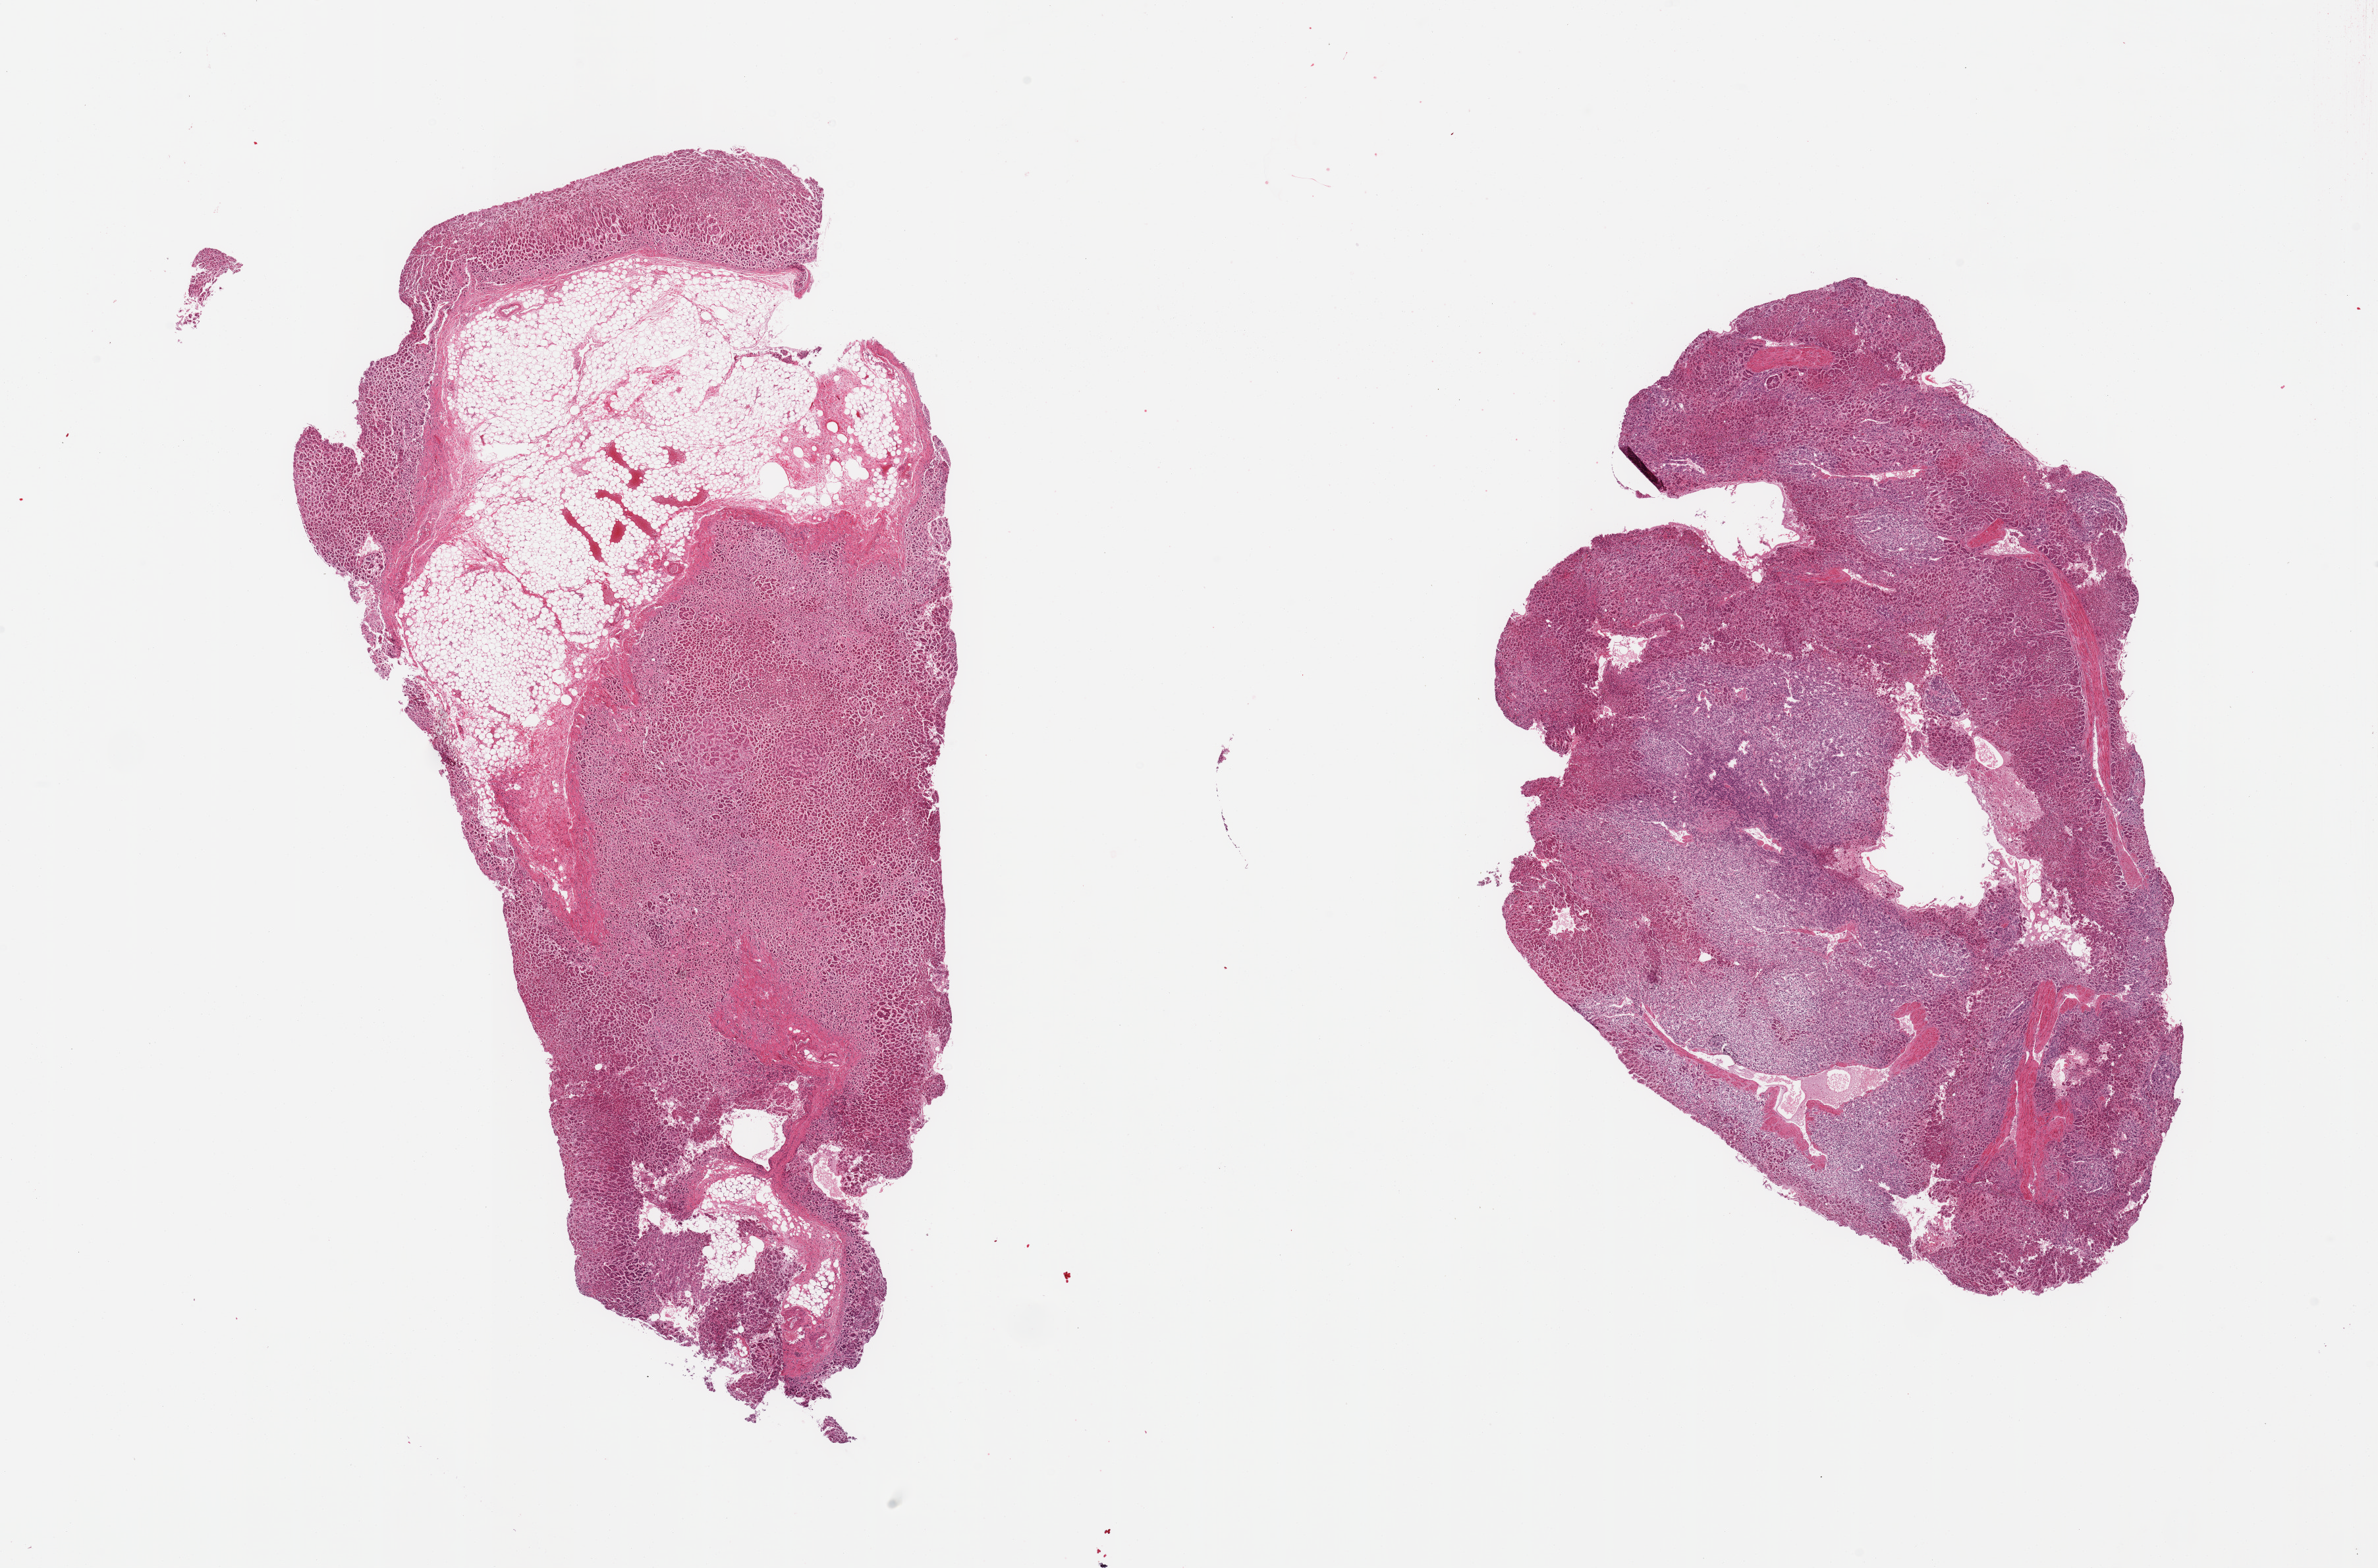
Haematoxylin and eosin whole-slide image, low-resolution overview of the scanned area, about 28.5 x 18.8 mm; PAXgene-fixed paraffin-embedded (PFPE) section; section of adrenal gland (target tissue); donor tissue sample.
Reviewer comment on this tissue sample: 2 pieces, cortex, ~20% adherent/interstitial fat.